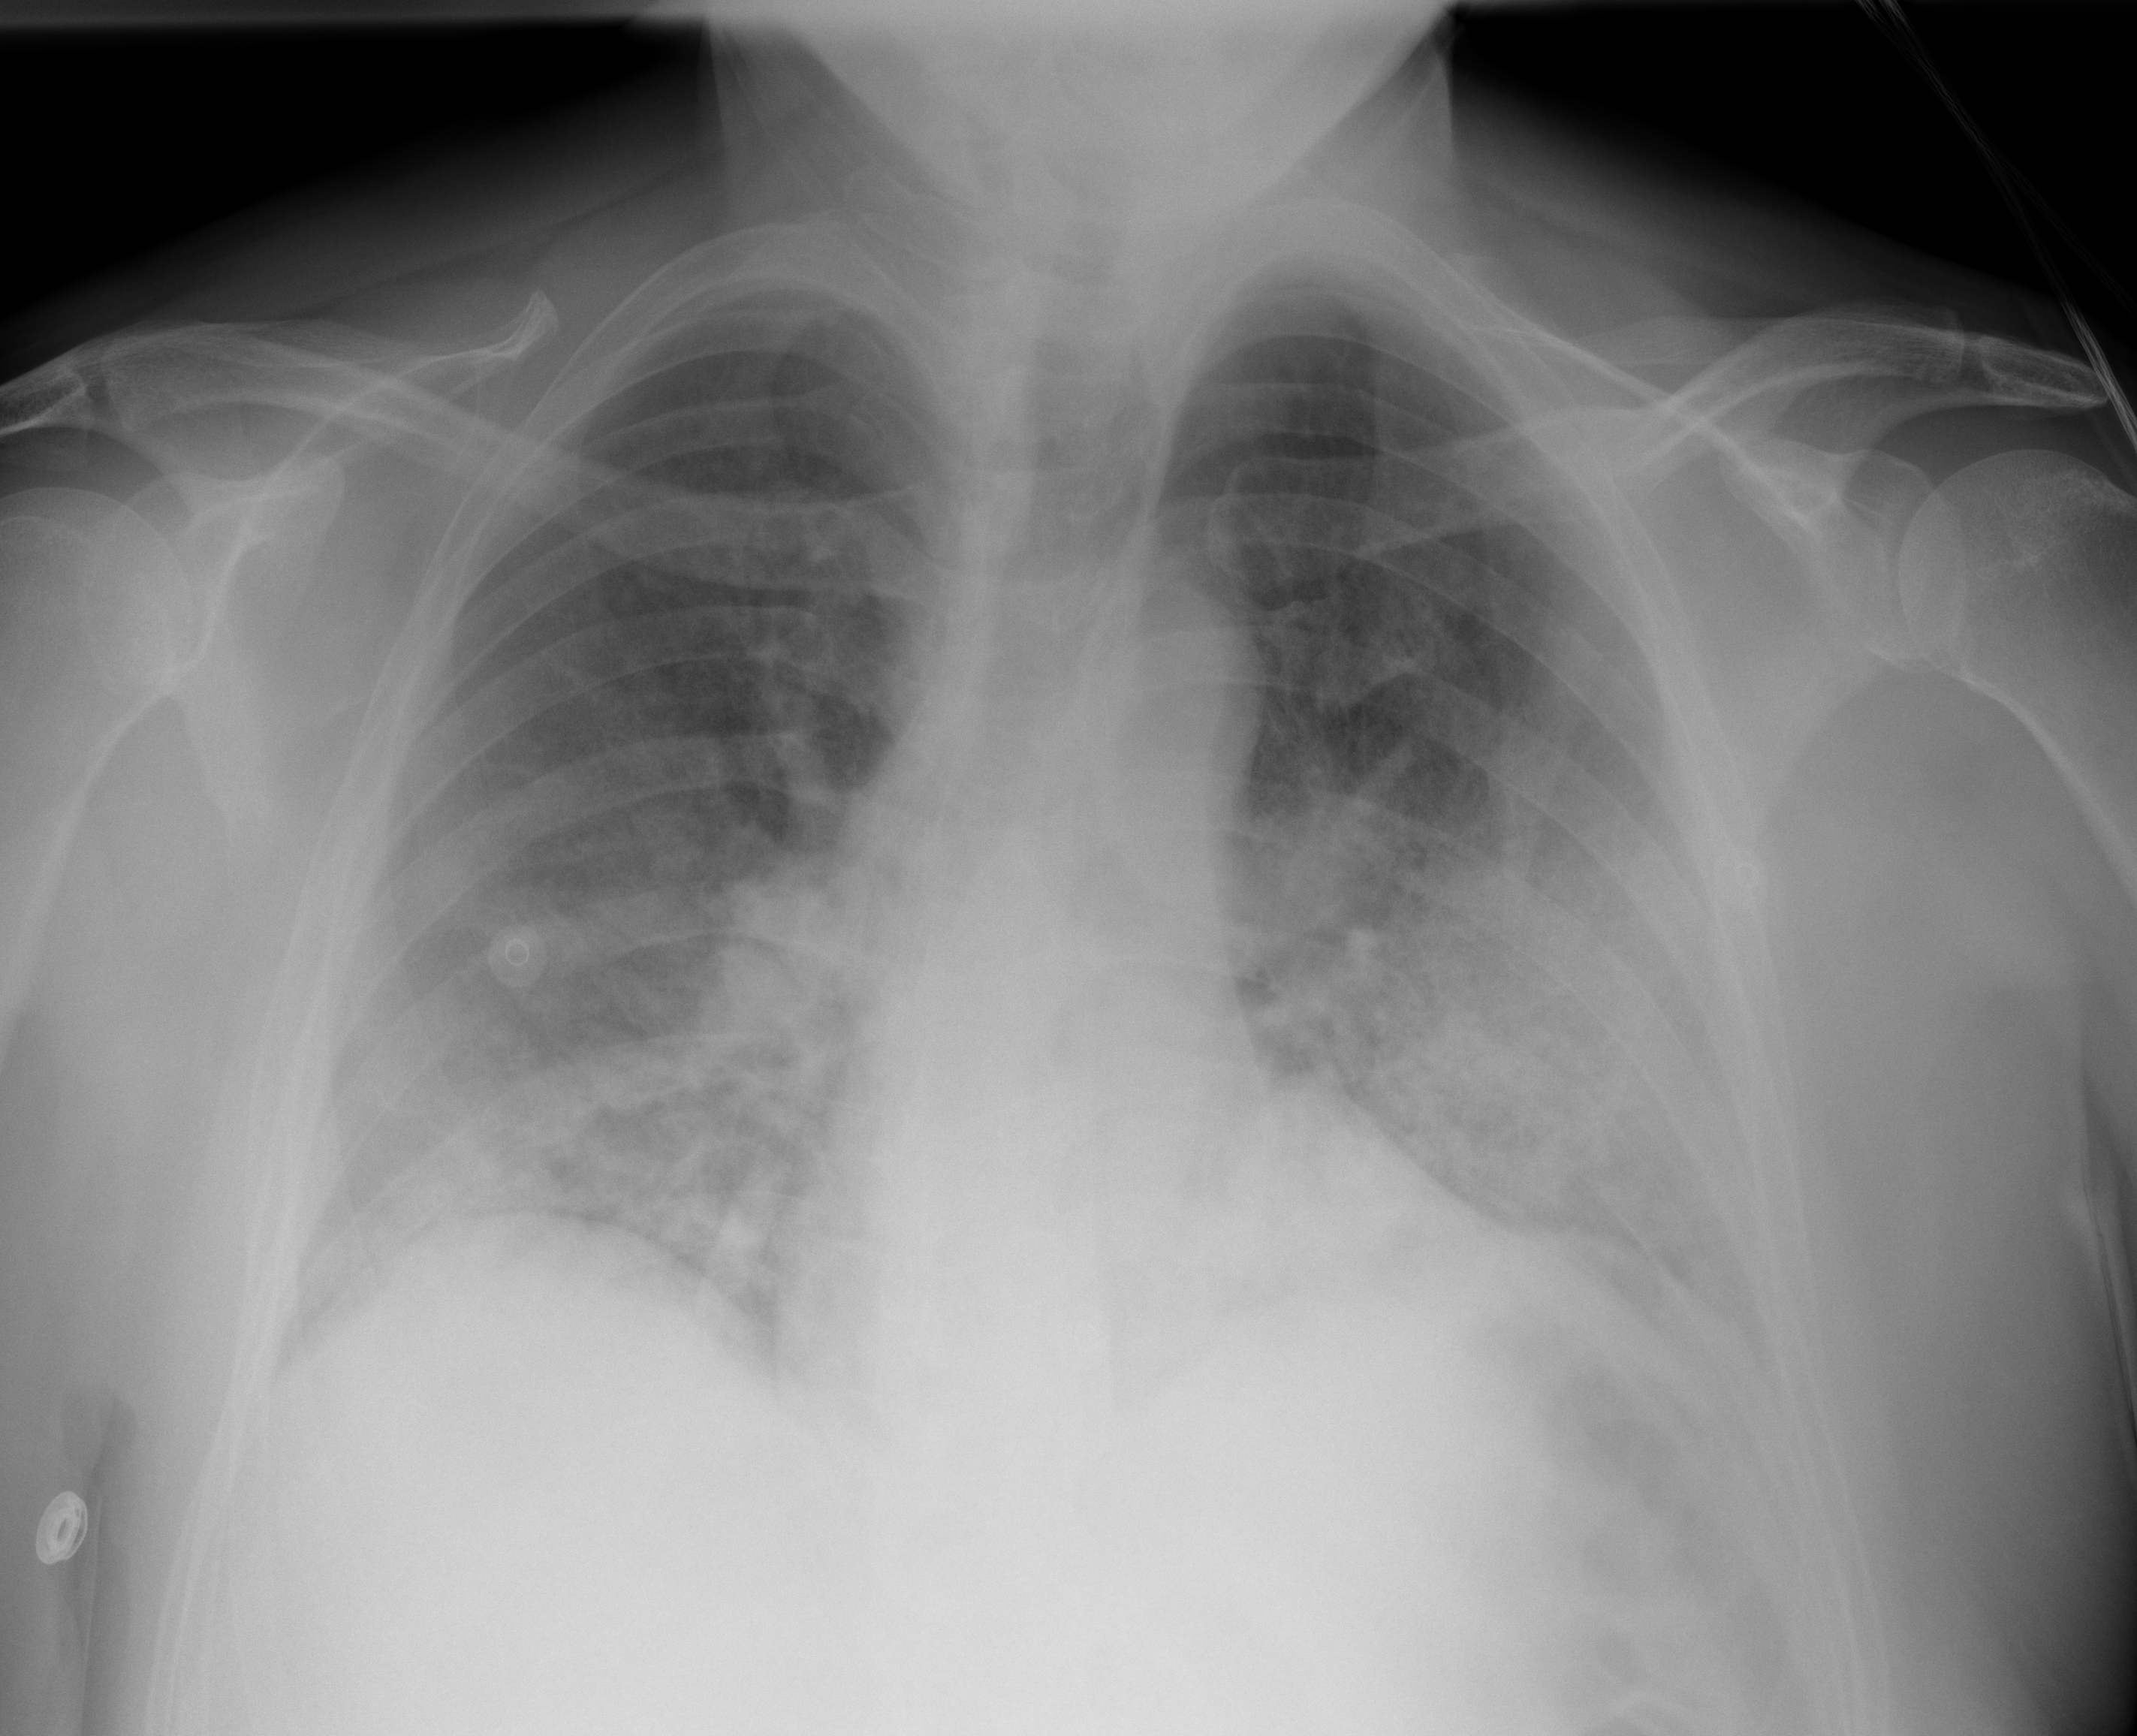
Chest X-ray (portable), AP projection. Male patient, age 57 years; imaged 0 days after the COVID-19 diagnosis.
Radiologist key findings (as recorded): There are bibasilar airspace opacities, left worse than right.